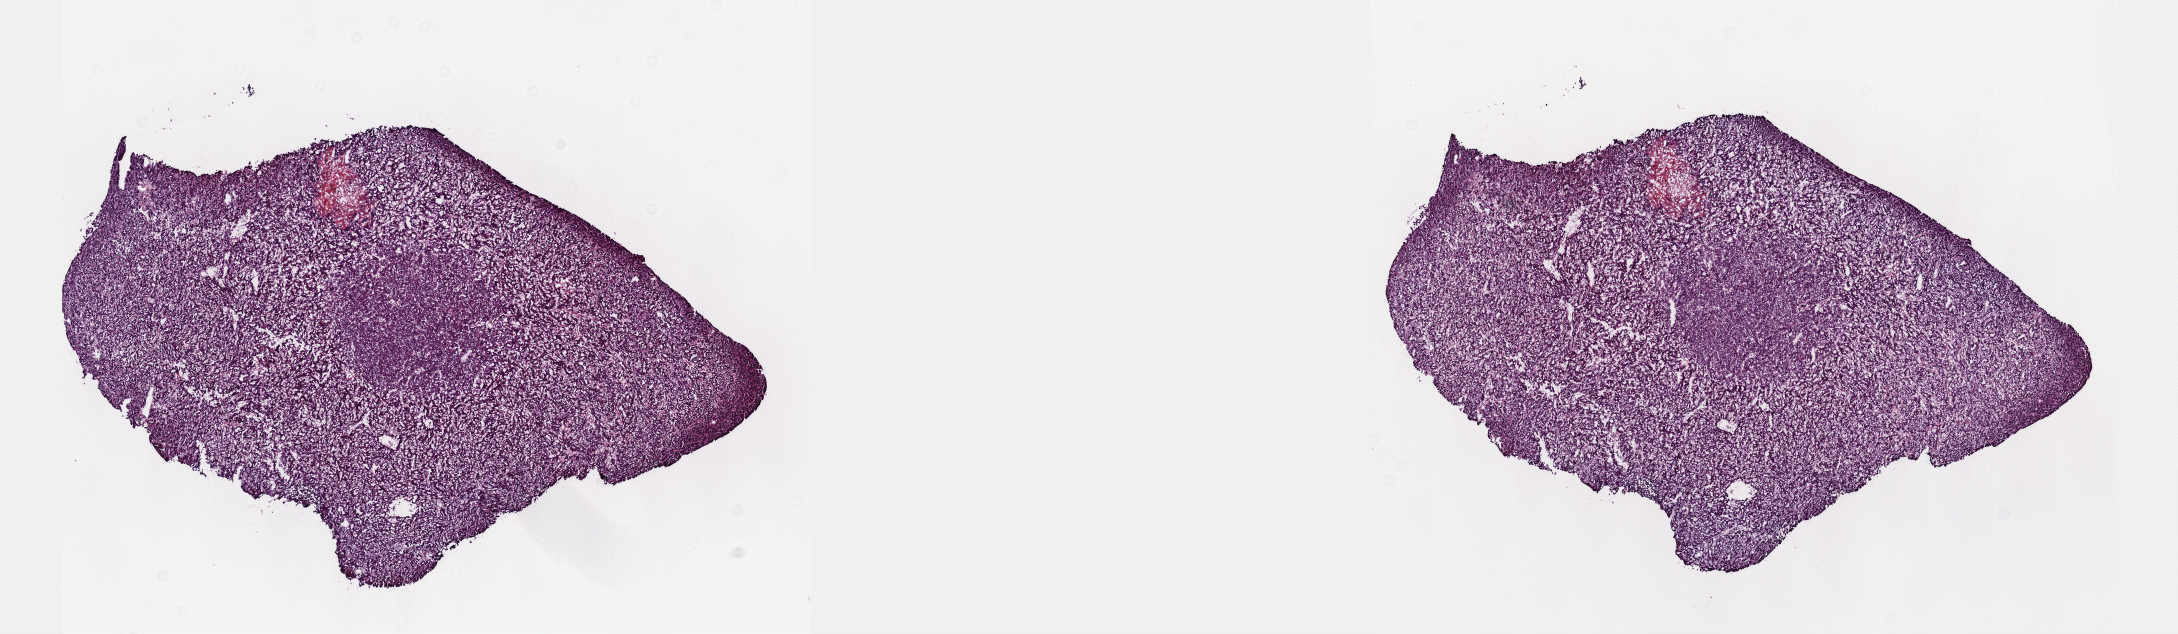
Digitized H&E-stained tissue section (whole slide) — low-resolution overview of the scanned area, about 17.6 x 5.1 mm, frozen section from the top of the tissue portion, sample: primary tumour, liver. Patient: male, age at initial diagnosis 63 years. Slide review estimates, as recorded: tumour cells 85%, tumour nuclei 95%.
Pathologic diagnosis: Hepatocellular carcinoma, NOS.